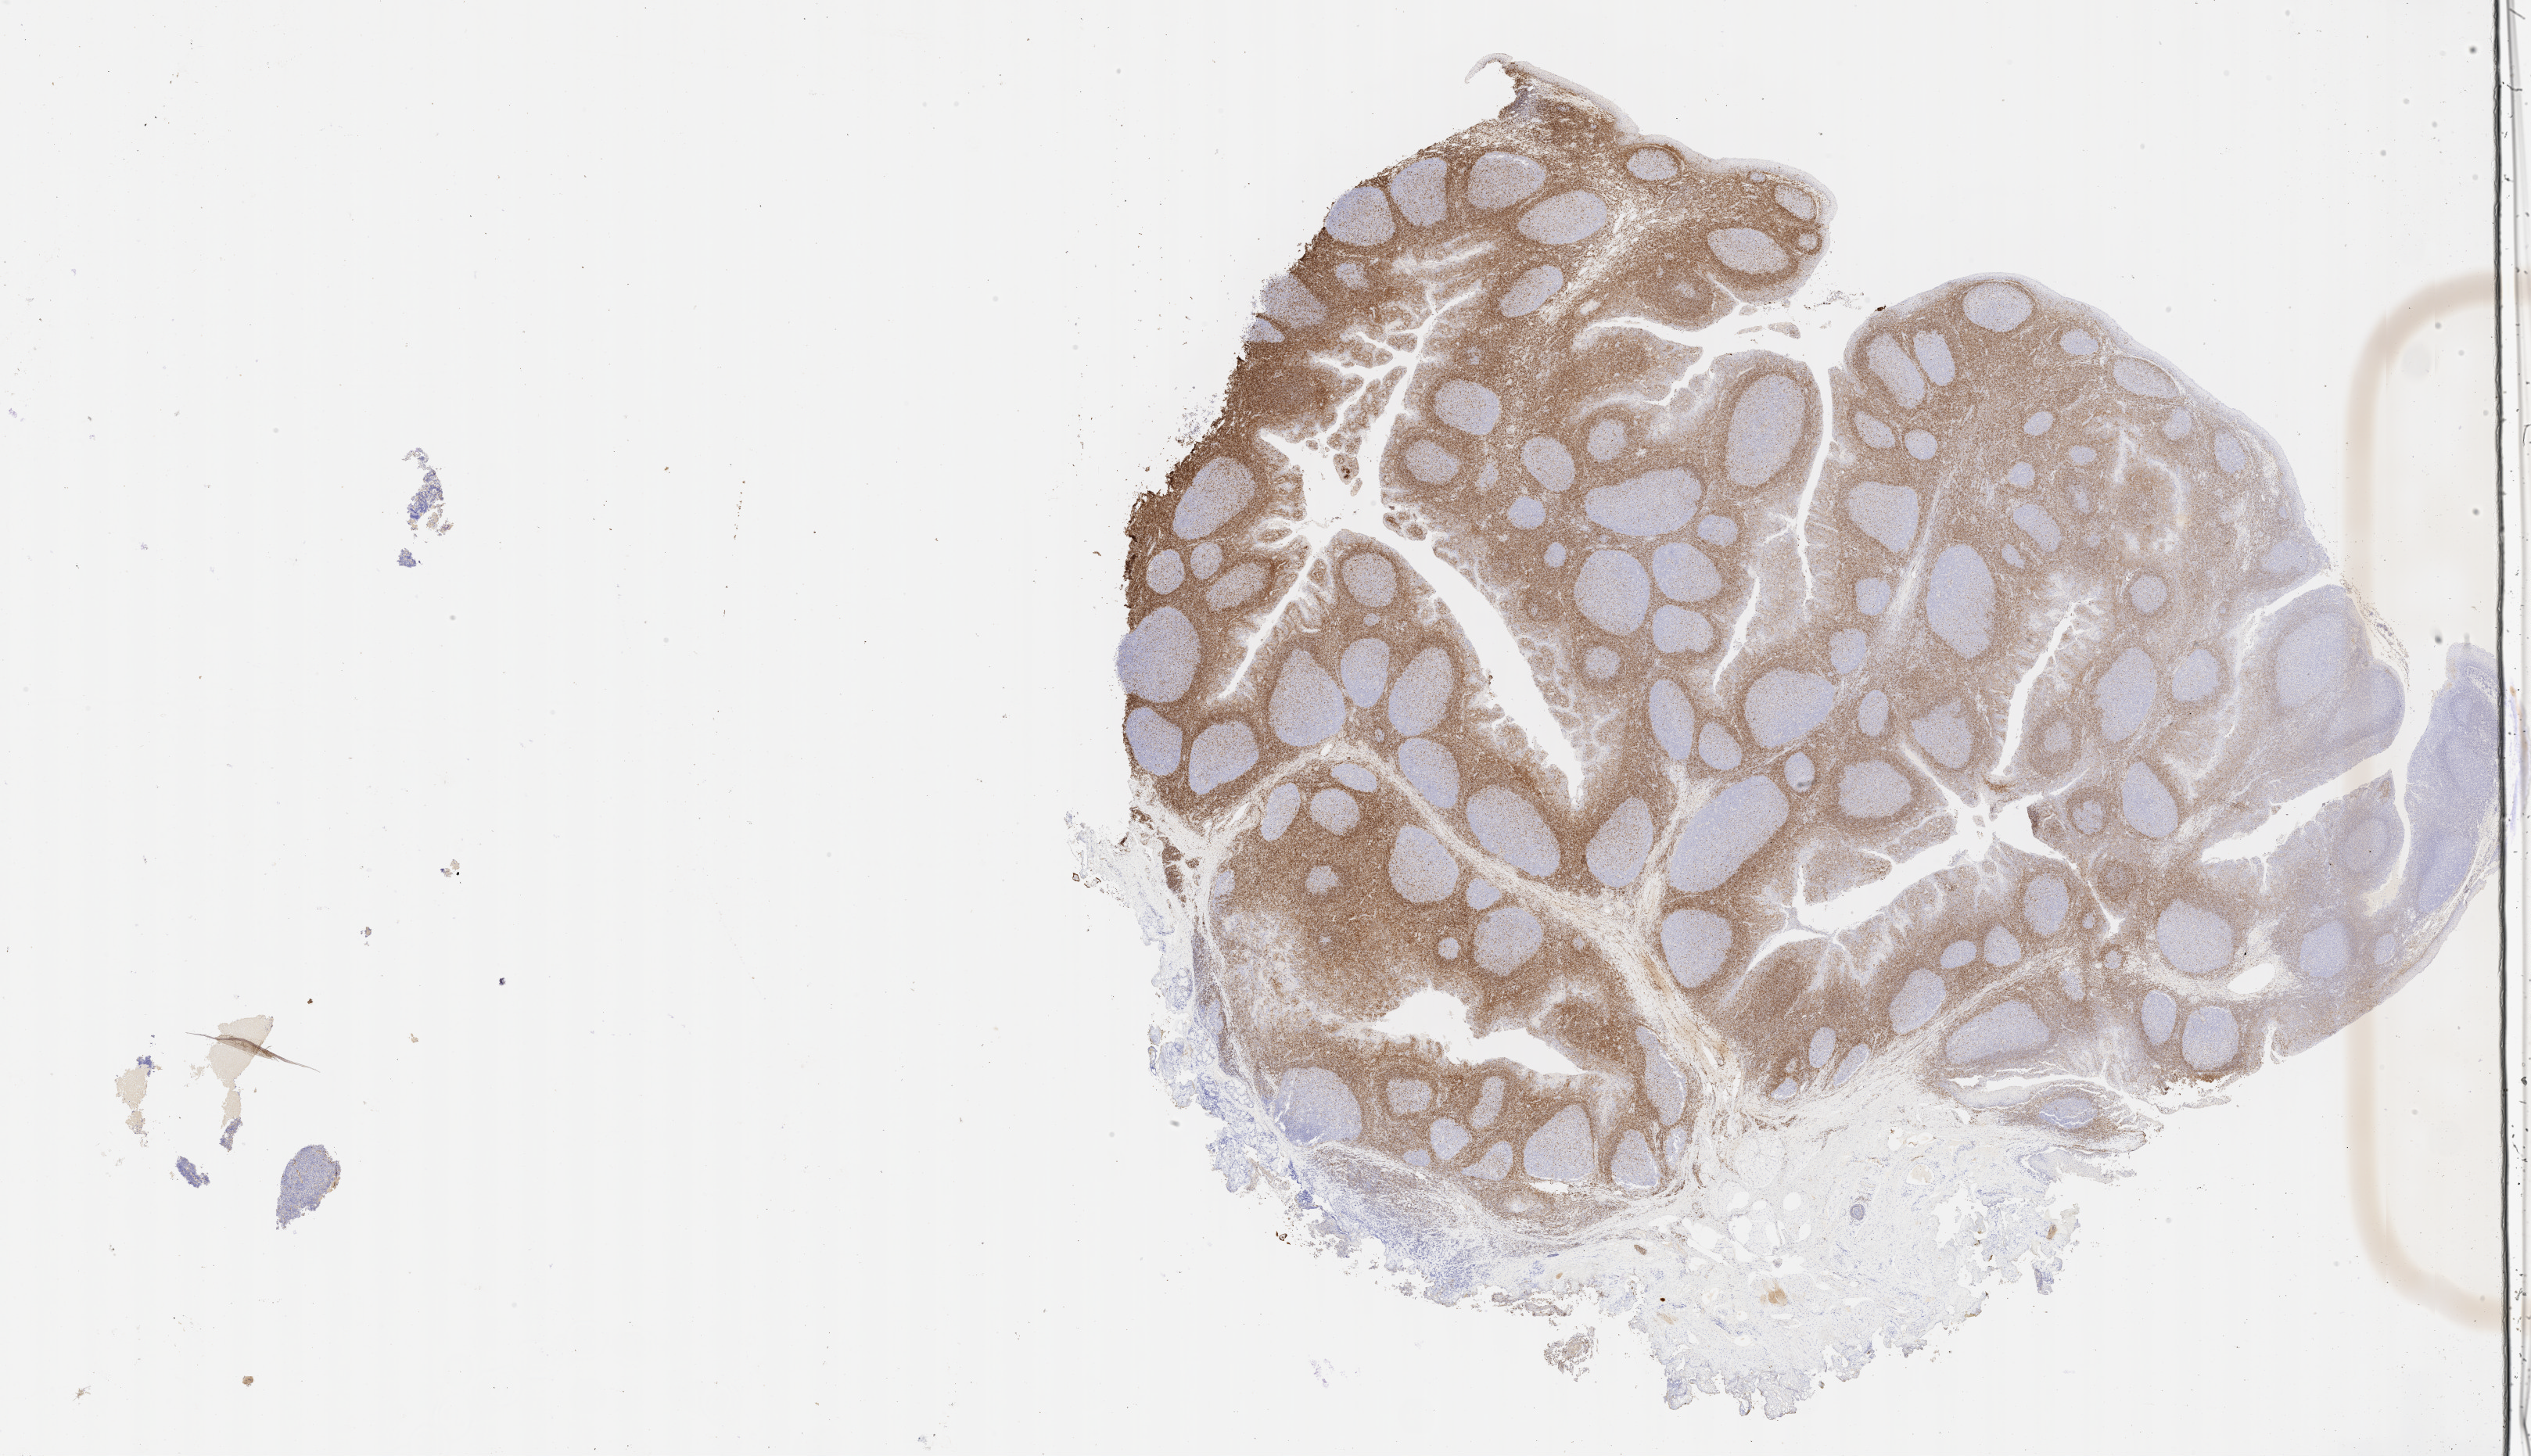
Whole-slide image, immunohistochemical stain for BCL2 — whole scanned area (about 26.2 x 15.1 mm) shown as a low-resolution overview; tumor tissue; anatomic site: abdominal lymph node. Male, age 5 years at initial diagnosis.
Diagnosis: Diffuse large B-cell lymphoma, NOS.